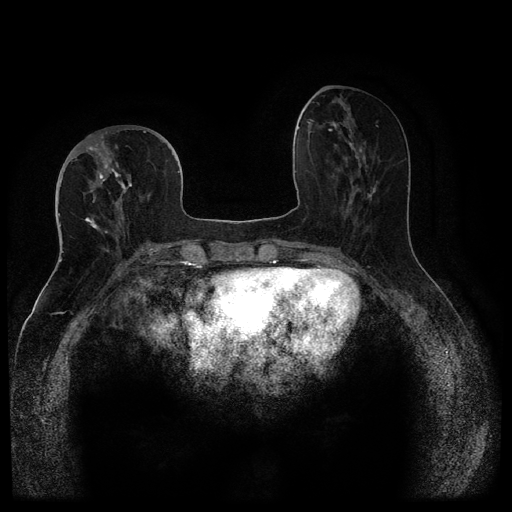
Breast MRI (dynamic contrast-enhanced, multi-phase), one axial slice; dynamic contrast-enhanced series, time point 2 of 5 at this slice position (early post-contrast); 1.5 T; TE 2.6 ms, TR 5.4 ms; 2 mm slice thickness; 512 × 512 image matrix, field of view 340 × 340 mm. Female patient, age 68 years.
Outlined on this slice (semi-automatically segmented with operator editing):
- breast lesion (labelled 'tumour' in the annotation; benign lesions carry a separate 'benign' label): bounding box (x1, y1, x2, y2) in pixels: (118, 177, 133, 197)